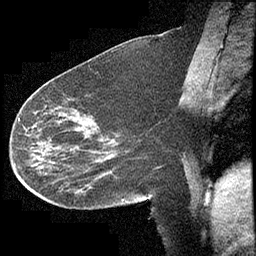
Breast MRI (dynamic contrast-enhanced), one sagittal slice; slice 177 of 232 in the series (ordered by position); dynamic contrast-enhanced study with each time point stored as its own series, time point 2 of 4 at this slice position (early post-contrast, ordered by acquisition time); 1.5 T; TE 4.2 ms, TR 6.7 ms; 3 mm slice thickness; 256 × 256 image matrix, field of view 200 × 200 mm. Female patient, age 63 years. Case-level facts recorded for this patient, not image findings: setting: breast cancer imaged before/during neoadjuvant chemotherapy; receptor status: triple-negative.
Annotated regions visible in this slice (semi-automatic segmentation, software-assisted and operator-edited):
- analysis volume of interest (the breast-tissue region the enhancement analysis was run in; not a lesion): bounding box <13,90,140,210> (left, top, right, bottom; pixels)
- tumour enhancement mask (voxels above the 70 % enhancement threshold inside the analysis volume of interest): <19,119,36,165>